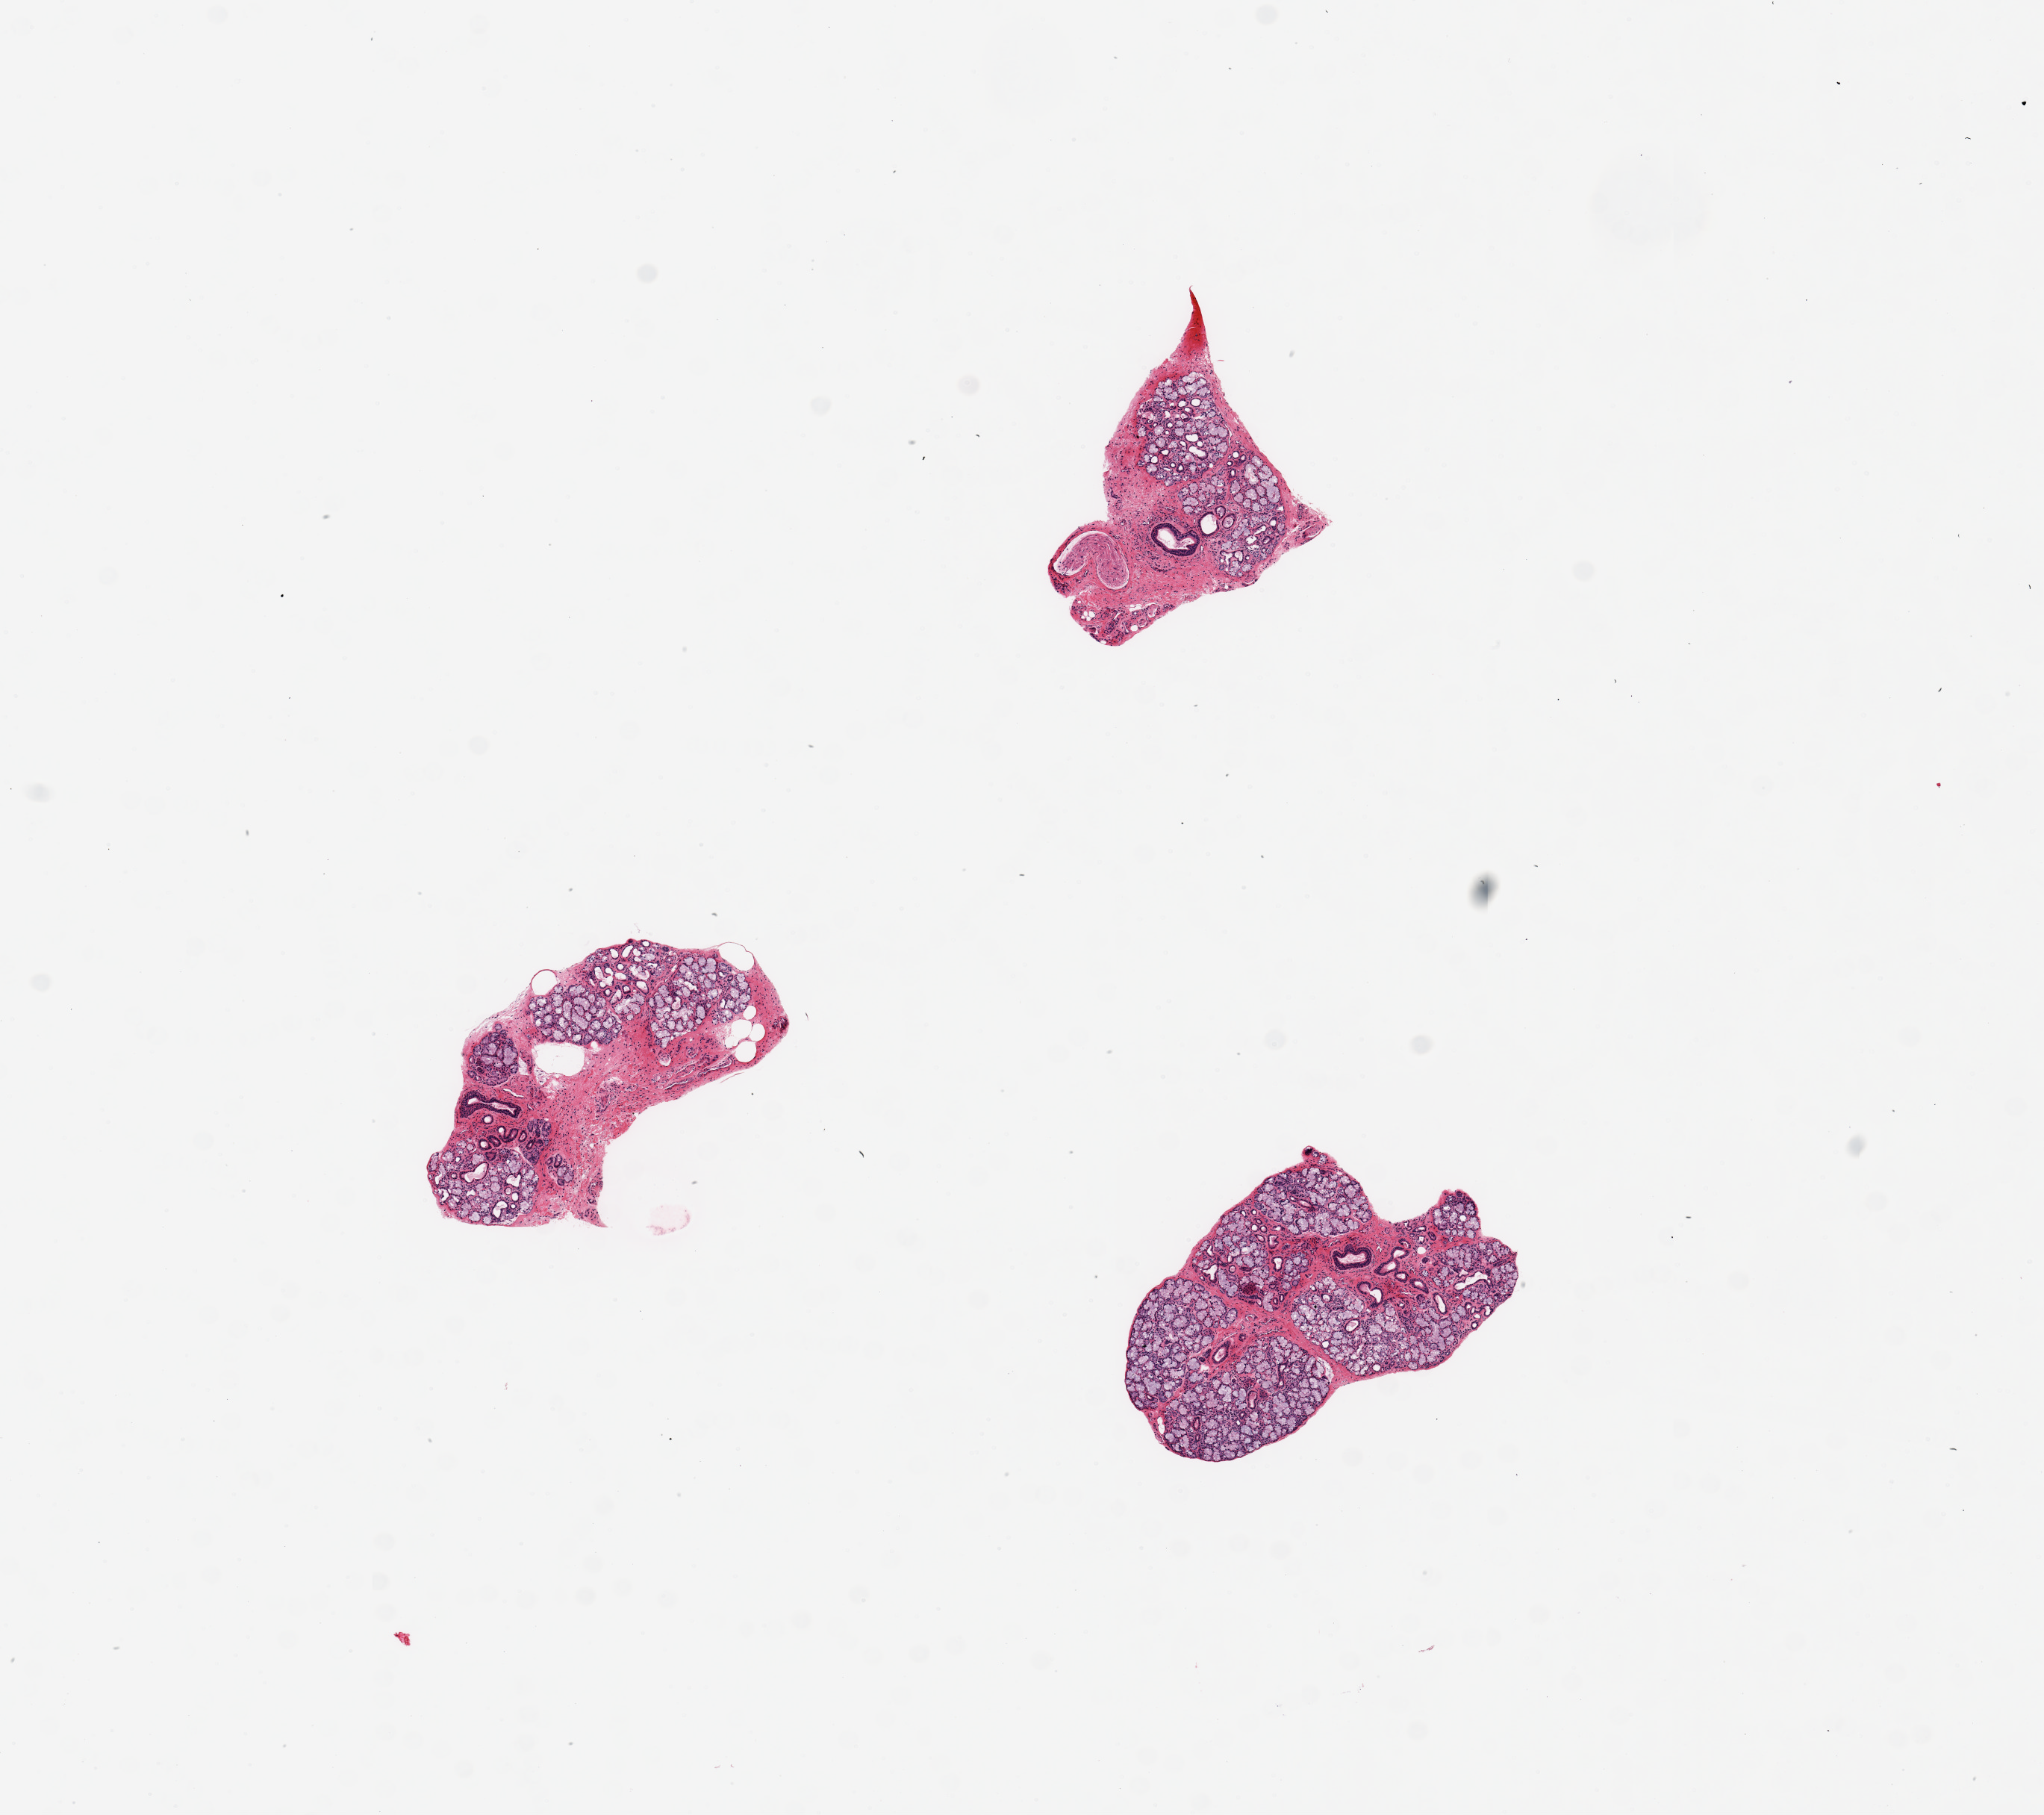
Whole-slide image, haematoxylin and eosin stain — shown as a low-resolution overview of the whole scanned area (about 10.8 x 9.6 mm, from a 20x scan), PAXgene-fixed paraffin-embedded (PFPE) section, target tissue: minor salivary gland, tissue donor sample. Donor: female.
Pathologist's review note for this sample: 3 pieces, up to 2x1mm;excellent specimen with good glands; 1 piece all glandular, 2 pieces with 50-60% glands, remainder stroma.